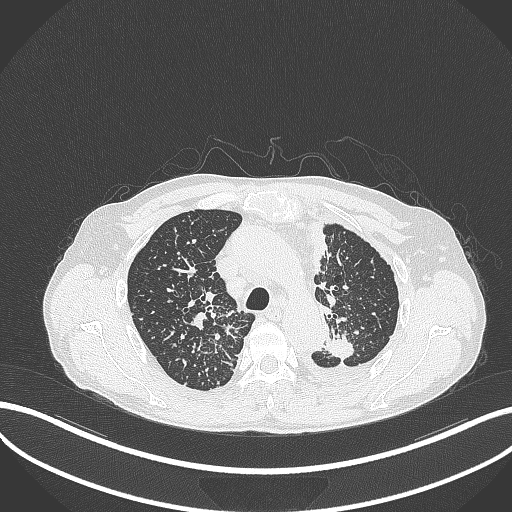
Chest CT, one axial slice; reconstruction kernel B70f; 120 kVp; lung window (W 1500 / L -600 HU); 1 mm slice thickness; 512 × 512 image matrix. Patient: male, 58 years. Case-level facts recorded for this patient, not image findings: clinical TNM (as recorded): T1c N3 M1.
Outlined on this slice (bounding box drawn by a radiologist):
- lung tumour (recorded histology: adenocarcinoma): box from (x=325, y=332) to (x=358, y=361) px